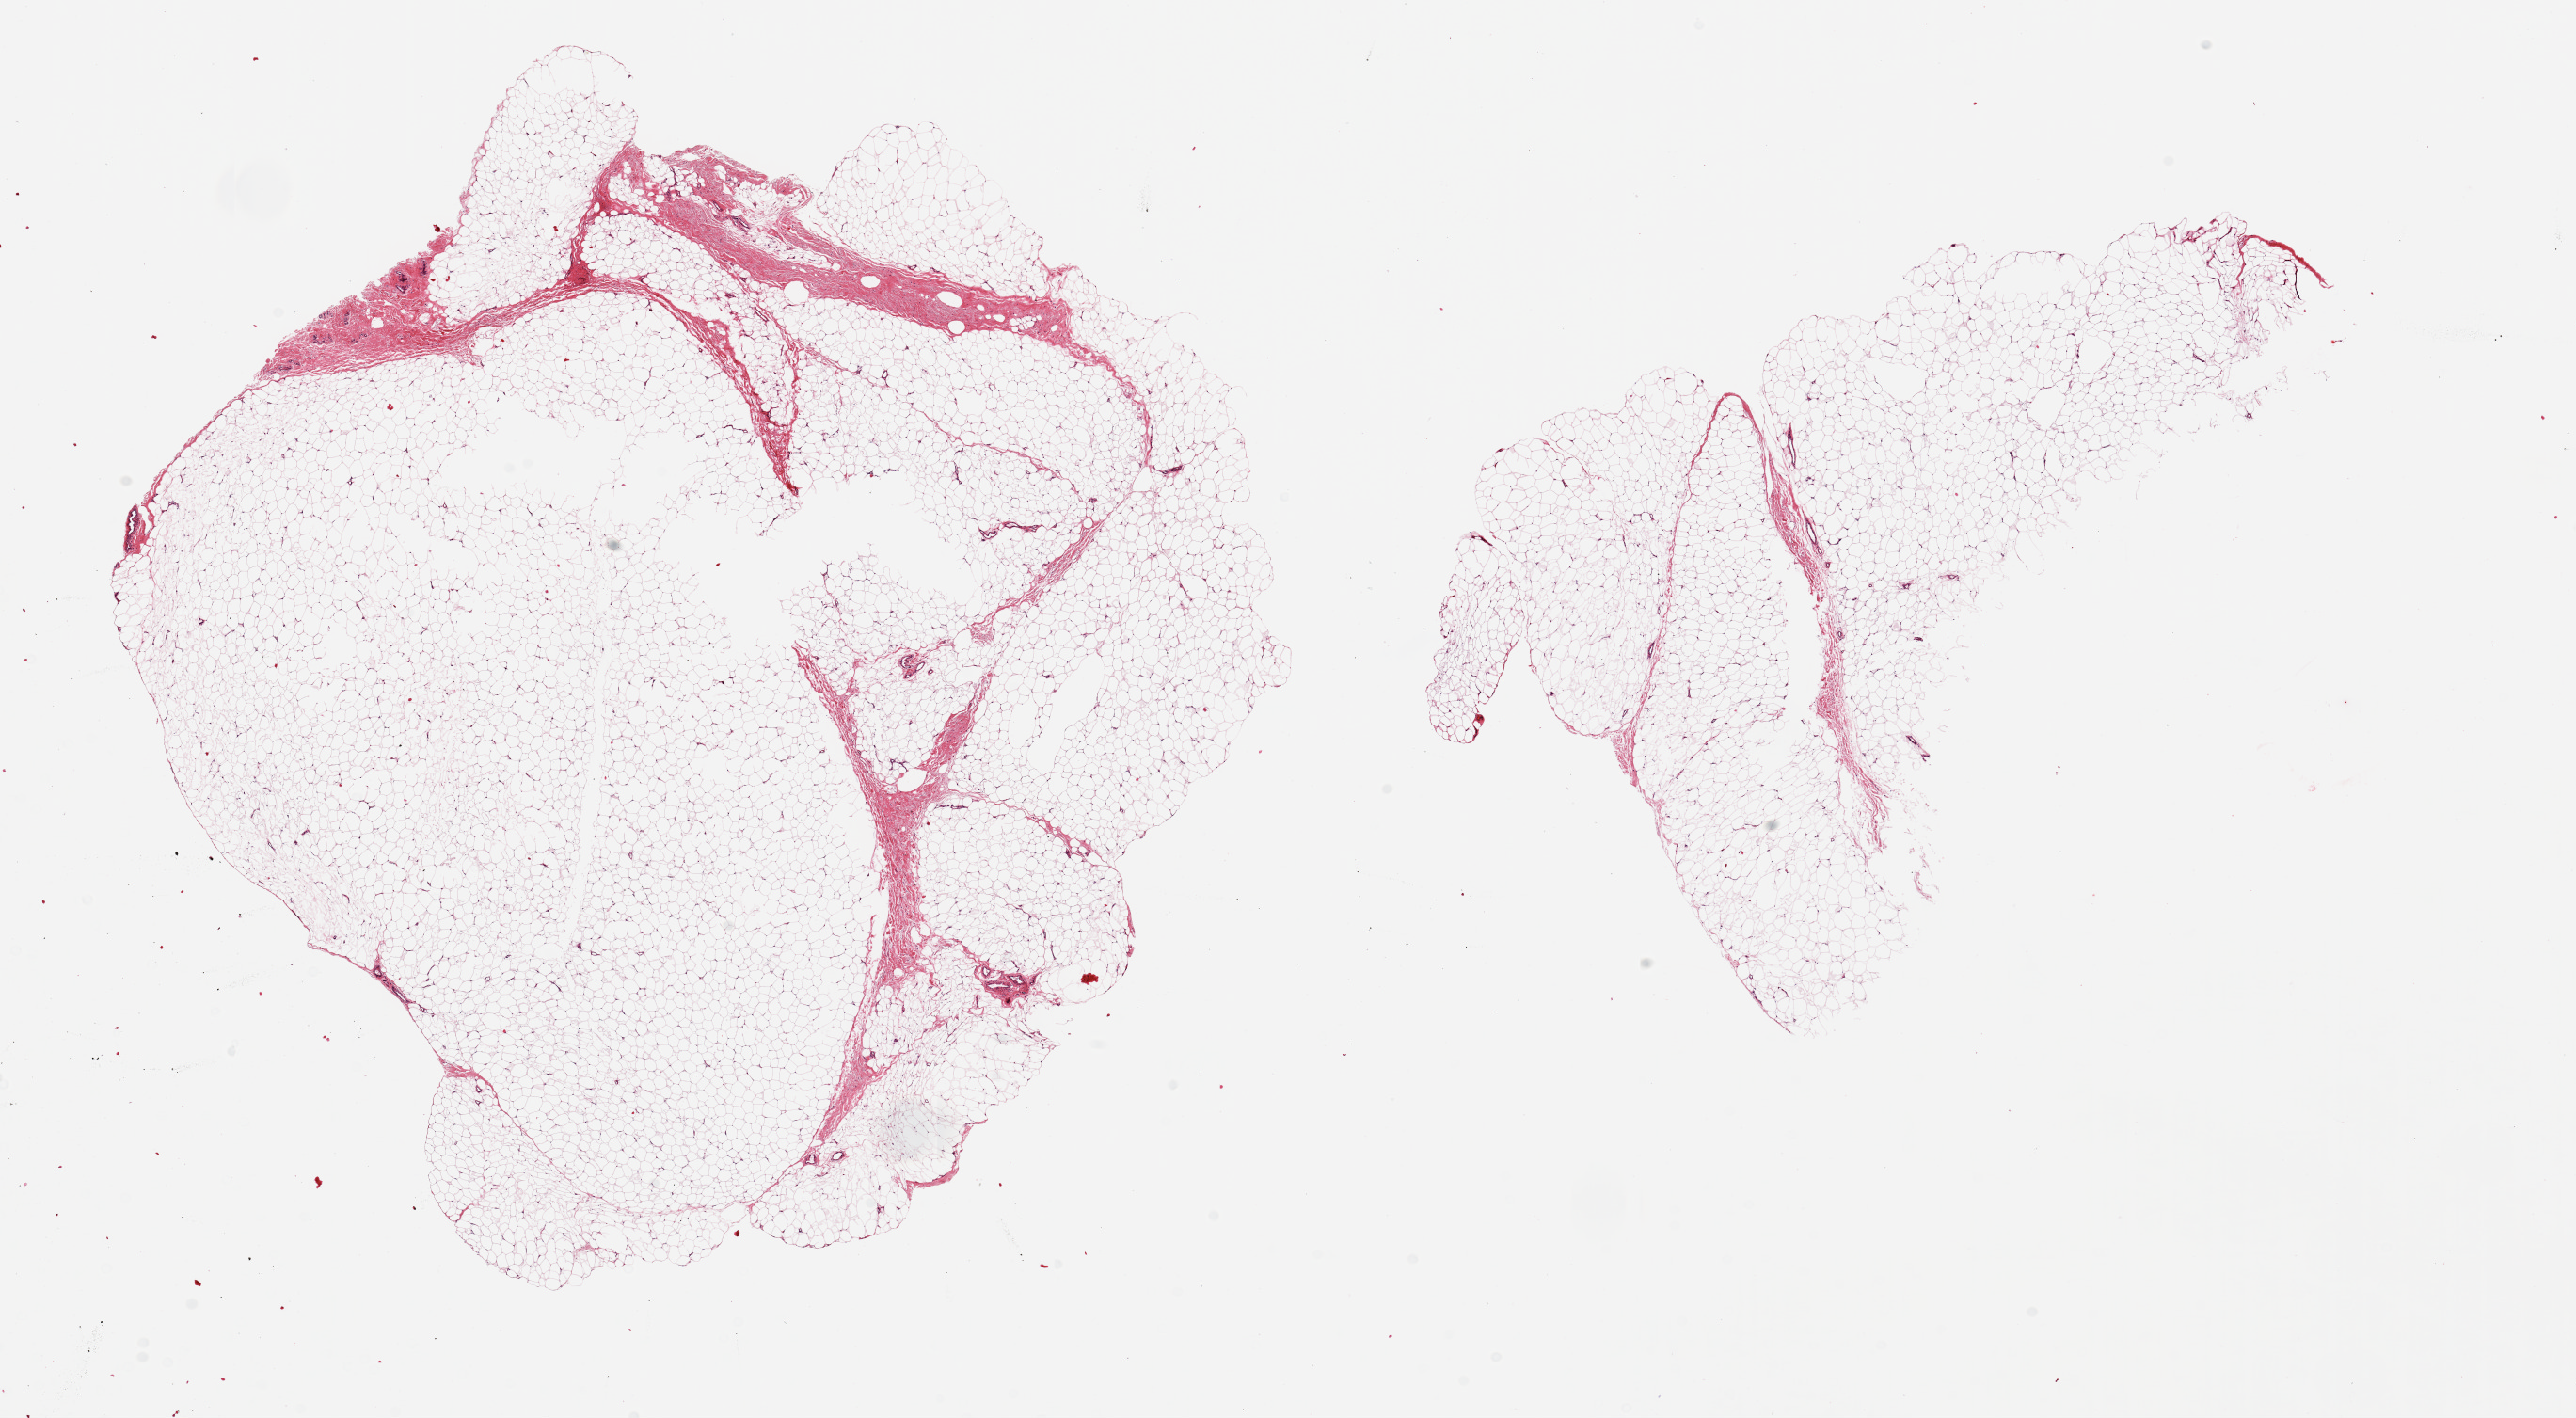
Hematoxylin and eosin (H&E) whole-slide image, brightfield — whole scanned area (about 21.7 x 11.9 mm) shown as a low-resolution overview, PAXgene-fixed paraffin-embedded (PFPE) section, sampled site (target tissue): adipose tissue, tissue donor sample. Male donor.
- review note (as recorded): 2 ~8x8mm aliquots